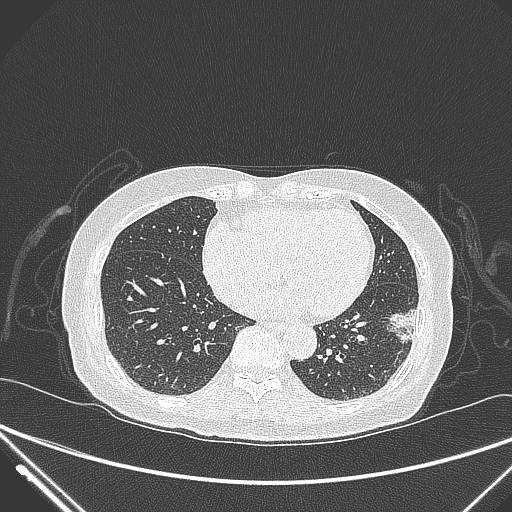
Chest CT, one axial slice. Slice 110 of 310 in the series (ordered by position). Lung window (W 1500 / L -600 HU). 1 mm slice thickness. 512 × 512 image matrix, field of view 377 × 377 mm. Female patient, age 82 years. From the clinical record (not read from this slice): clinical TNM (as recorded): T1c N0 M0; histopathological grade: G2.
Outlined on this slice (bounding box drawn by a radiologist):
- lung tumour (recorded histology: adenocarcinoma): box from (x=386, y=301) to (x=434, y=359) px